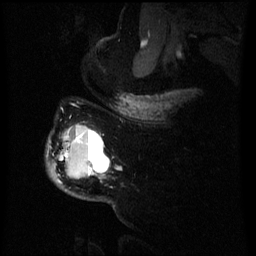
Breast MRI (dynamic contrast-enhanced), one sagittal slice. Dynamic contrast-enhanced series, image 2 of 3 at this slice position (ordered by acquisition). 1.5 T. TE 4.2 ms, TR 8 ms. 256 × 256 image matrix, field of view 200 × 200 mm. Patient: female, 50 years.
Annotated regions visible in this slice (semi-automatically segmented with operator editing):
- analysis volume of interest (the breast-tissue region the enhancement analysis was run in; not a lesion): bounding box [x1, y1, x2, y2] px = [50, 126, 110, 183]
- tumour enhancement mask (voxels above the 70 % enhancement threshold inside the analysis volume of interest): [75, 136, 94, 175]